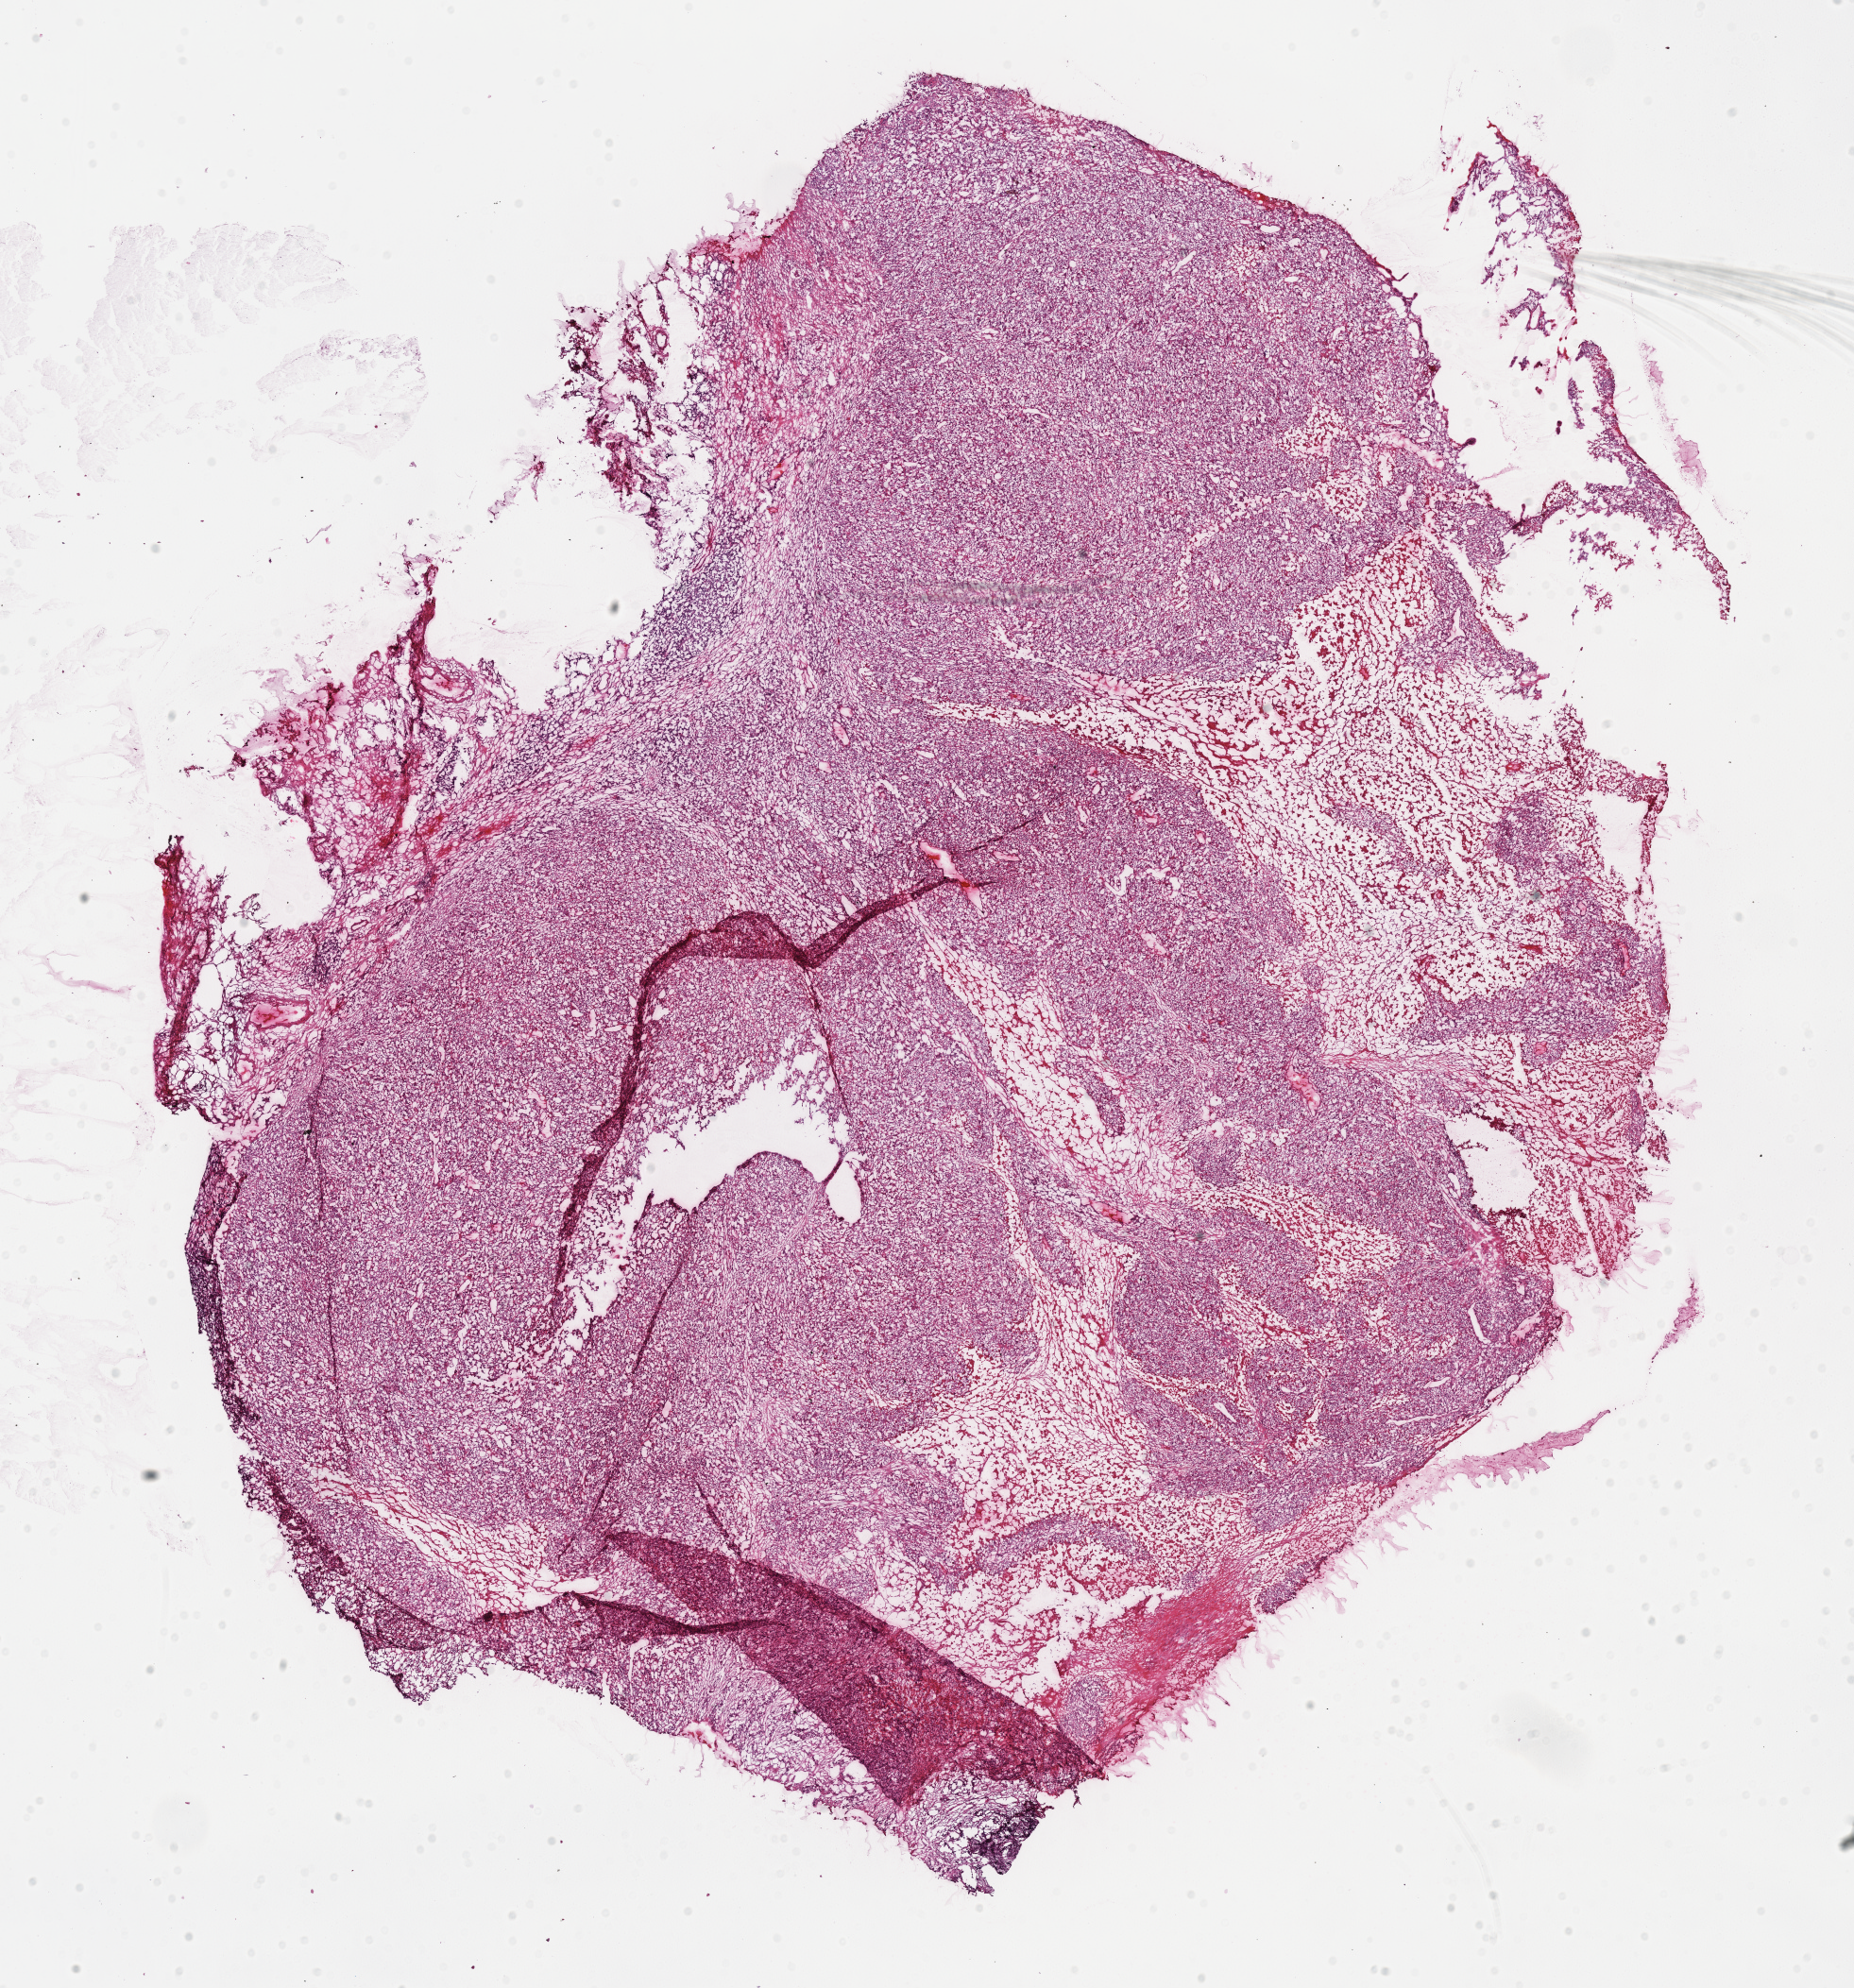
Digitized Hematoxylin and eosin (H&E) stained tissue section (whole slide) — a low-resolution overview of the entire scanned area, about 15.5 x 16.6 mm (slide scanned at 40x); frozen section; primary tumour sample from the lung. Patient: female, age at initial diagnosis 40 years. Slide review estimates, as recorded: tumour cells 75%, tumour nuclei 75%, normal cells 0%, stromal cells 10%, necrosis 15%.
• AJCC pathologic stage: IV (6th edition)
• histologic diagnosis: Adenocarcinoma, NOS (upper lobe, lung)